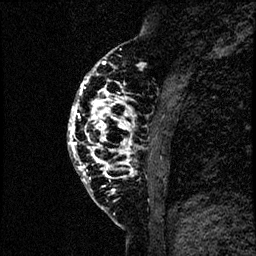
Breast MRI (dynamic contrast-enhanced), one sagittal slice; position 24 of 60 along the scan axis; dynamic contrast-enhanced study with each time point stored as its own series, time point 2 of 4 at this slice position (early post-contrast, ordered by acquisition time); 1.5 T; TE 4.2 ms, TR 17.6 ms; 2 mm slice thickness; 256 × 256 image matrix, field of view 200 × 200 mm. Female patient, age 40 years. Case-level facts recorded for this patient, not image findings: setting: breast cancer imaged before/during neoadjuvant chemotherapy; receptor status: HER2-positive.
Outlined on this slice (semi-automatically segmented with operator editing):
- analysis volume of interest (the breast-tissue region the enhancement analysis was run in; not a lesion): box from (x=66, y=55) to (x=185, y=206) px
- tumour enhancement mask (voxels above the 100 % enhancement threshold inside the analysis volume of interest): (x=68, y=61)–(x=130, y=183)